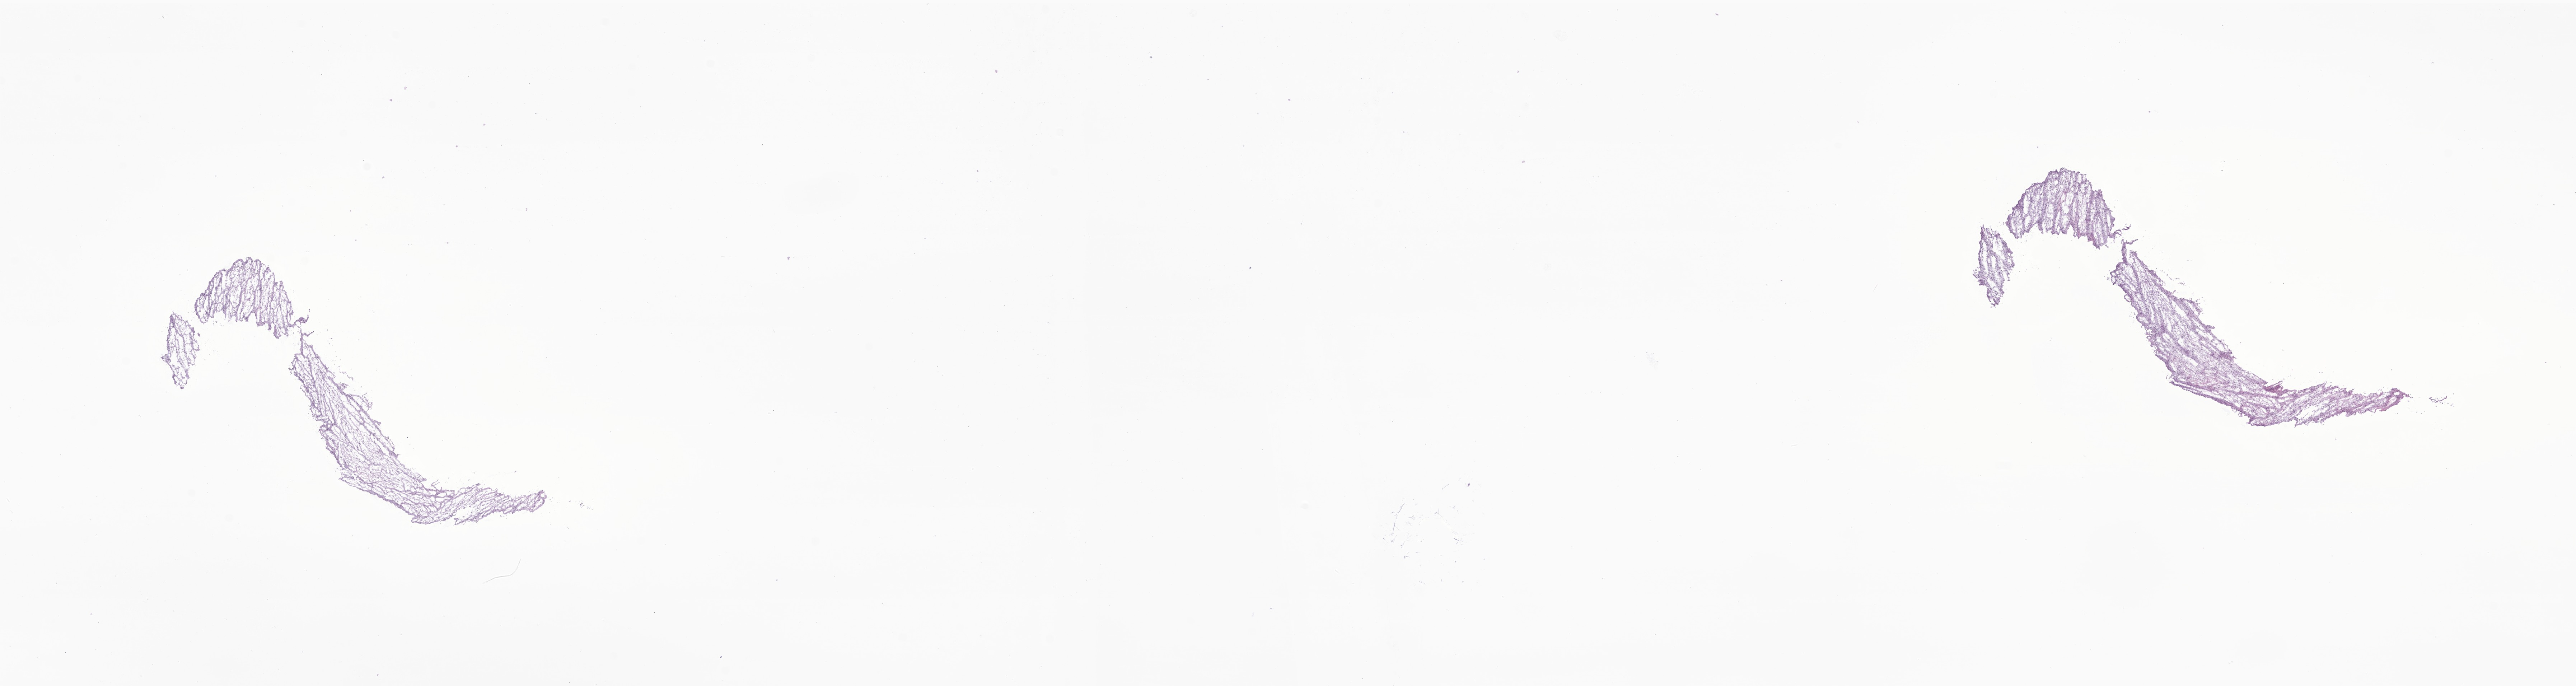
Digitized hematoxylin and eosin (H&E)-stained section of tumor tissue from the soft tissue of thorax, whole scanned area (about 30.3 x 8.1 mm) shown as a low-resolution overview. Frozen section. Patient female; age 131 months (10 years 11 months).
Diagnosis (ICD-O-3 morphology term): Spindle cell rhabdomyosarcoma.